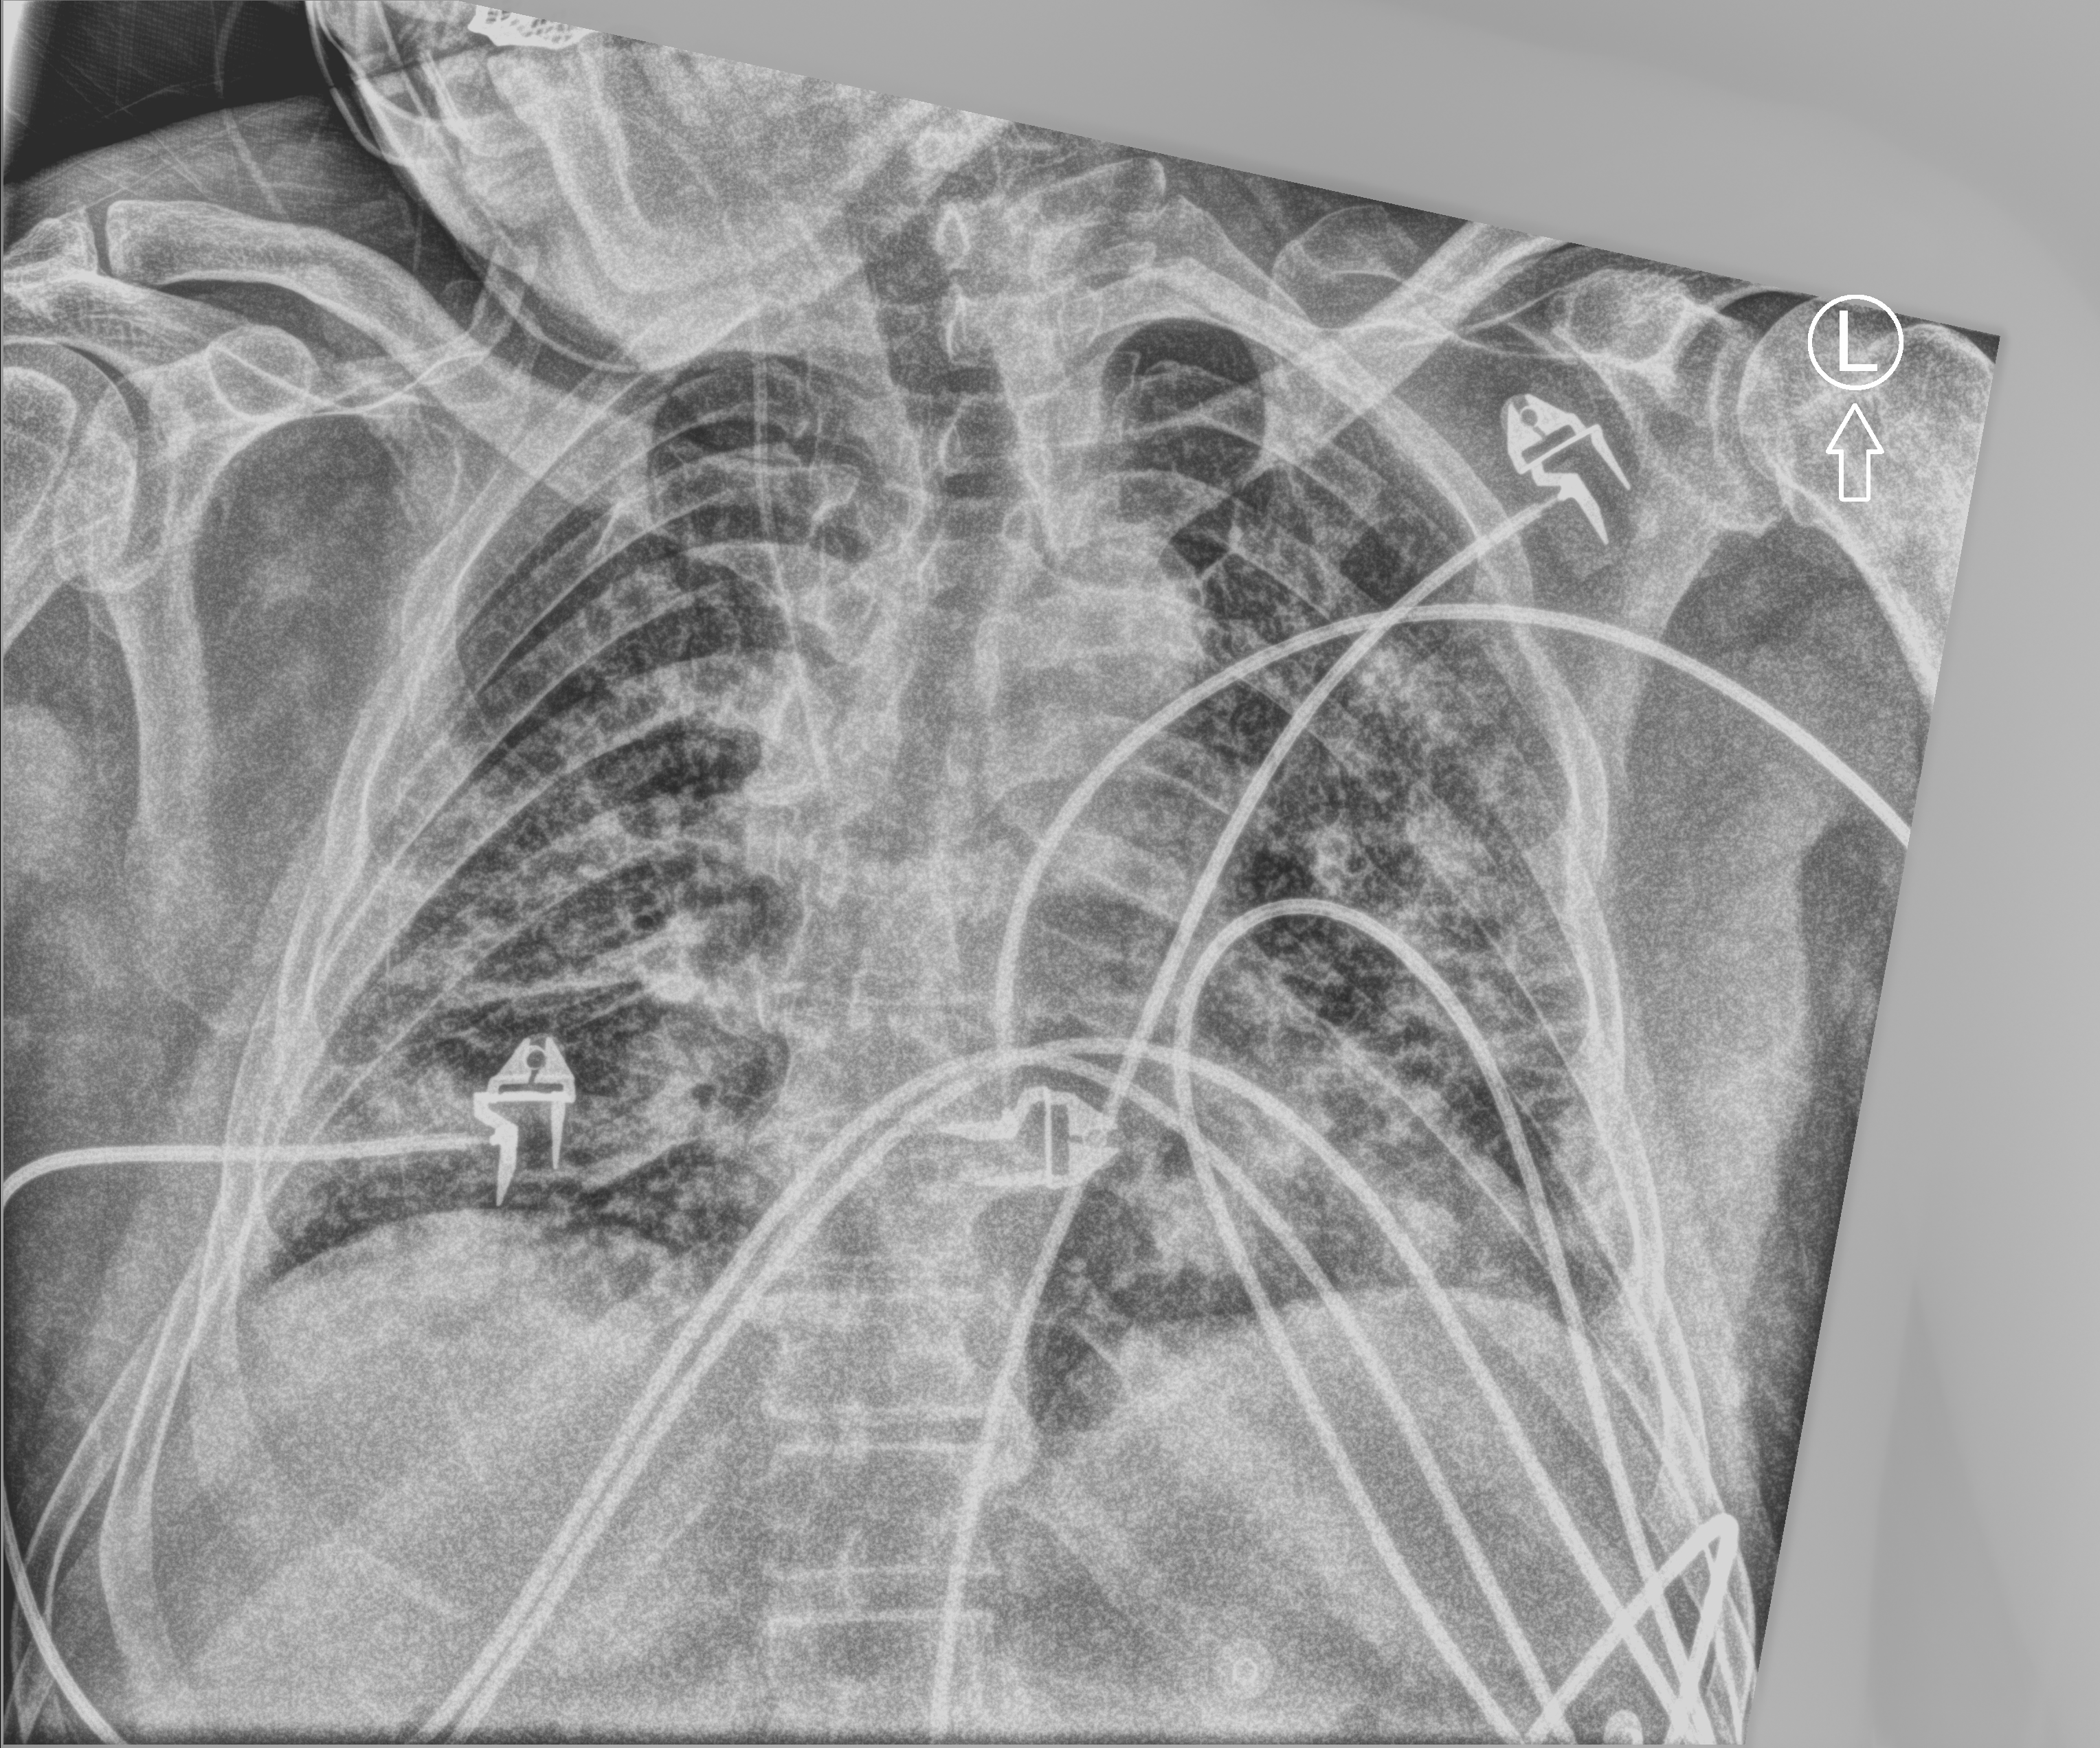
Portable chest radiograph, anteroposterior (AP) projection. Patient hospitalised with COVID-19; male, aged 60–74 years.
Hospital-stay facts (about this admission, not read from this image; timing relative to this image not recorded): length of hospital stay: 32 days; mechanically ventilated during this hospital stay: yes.